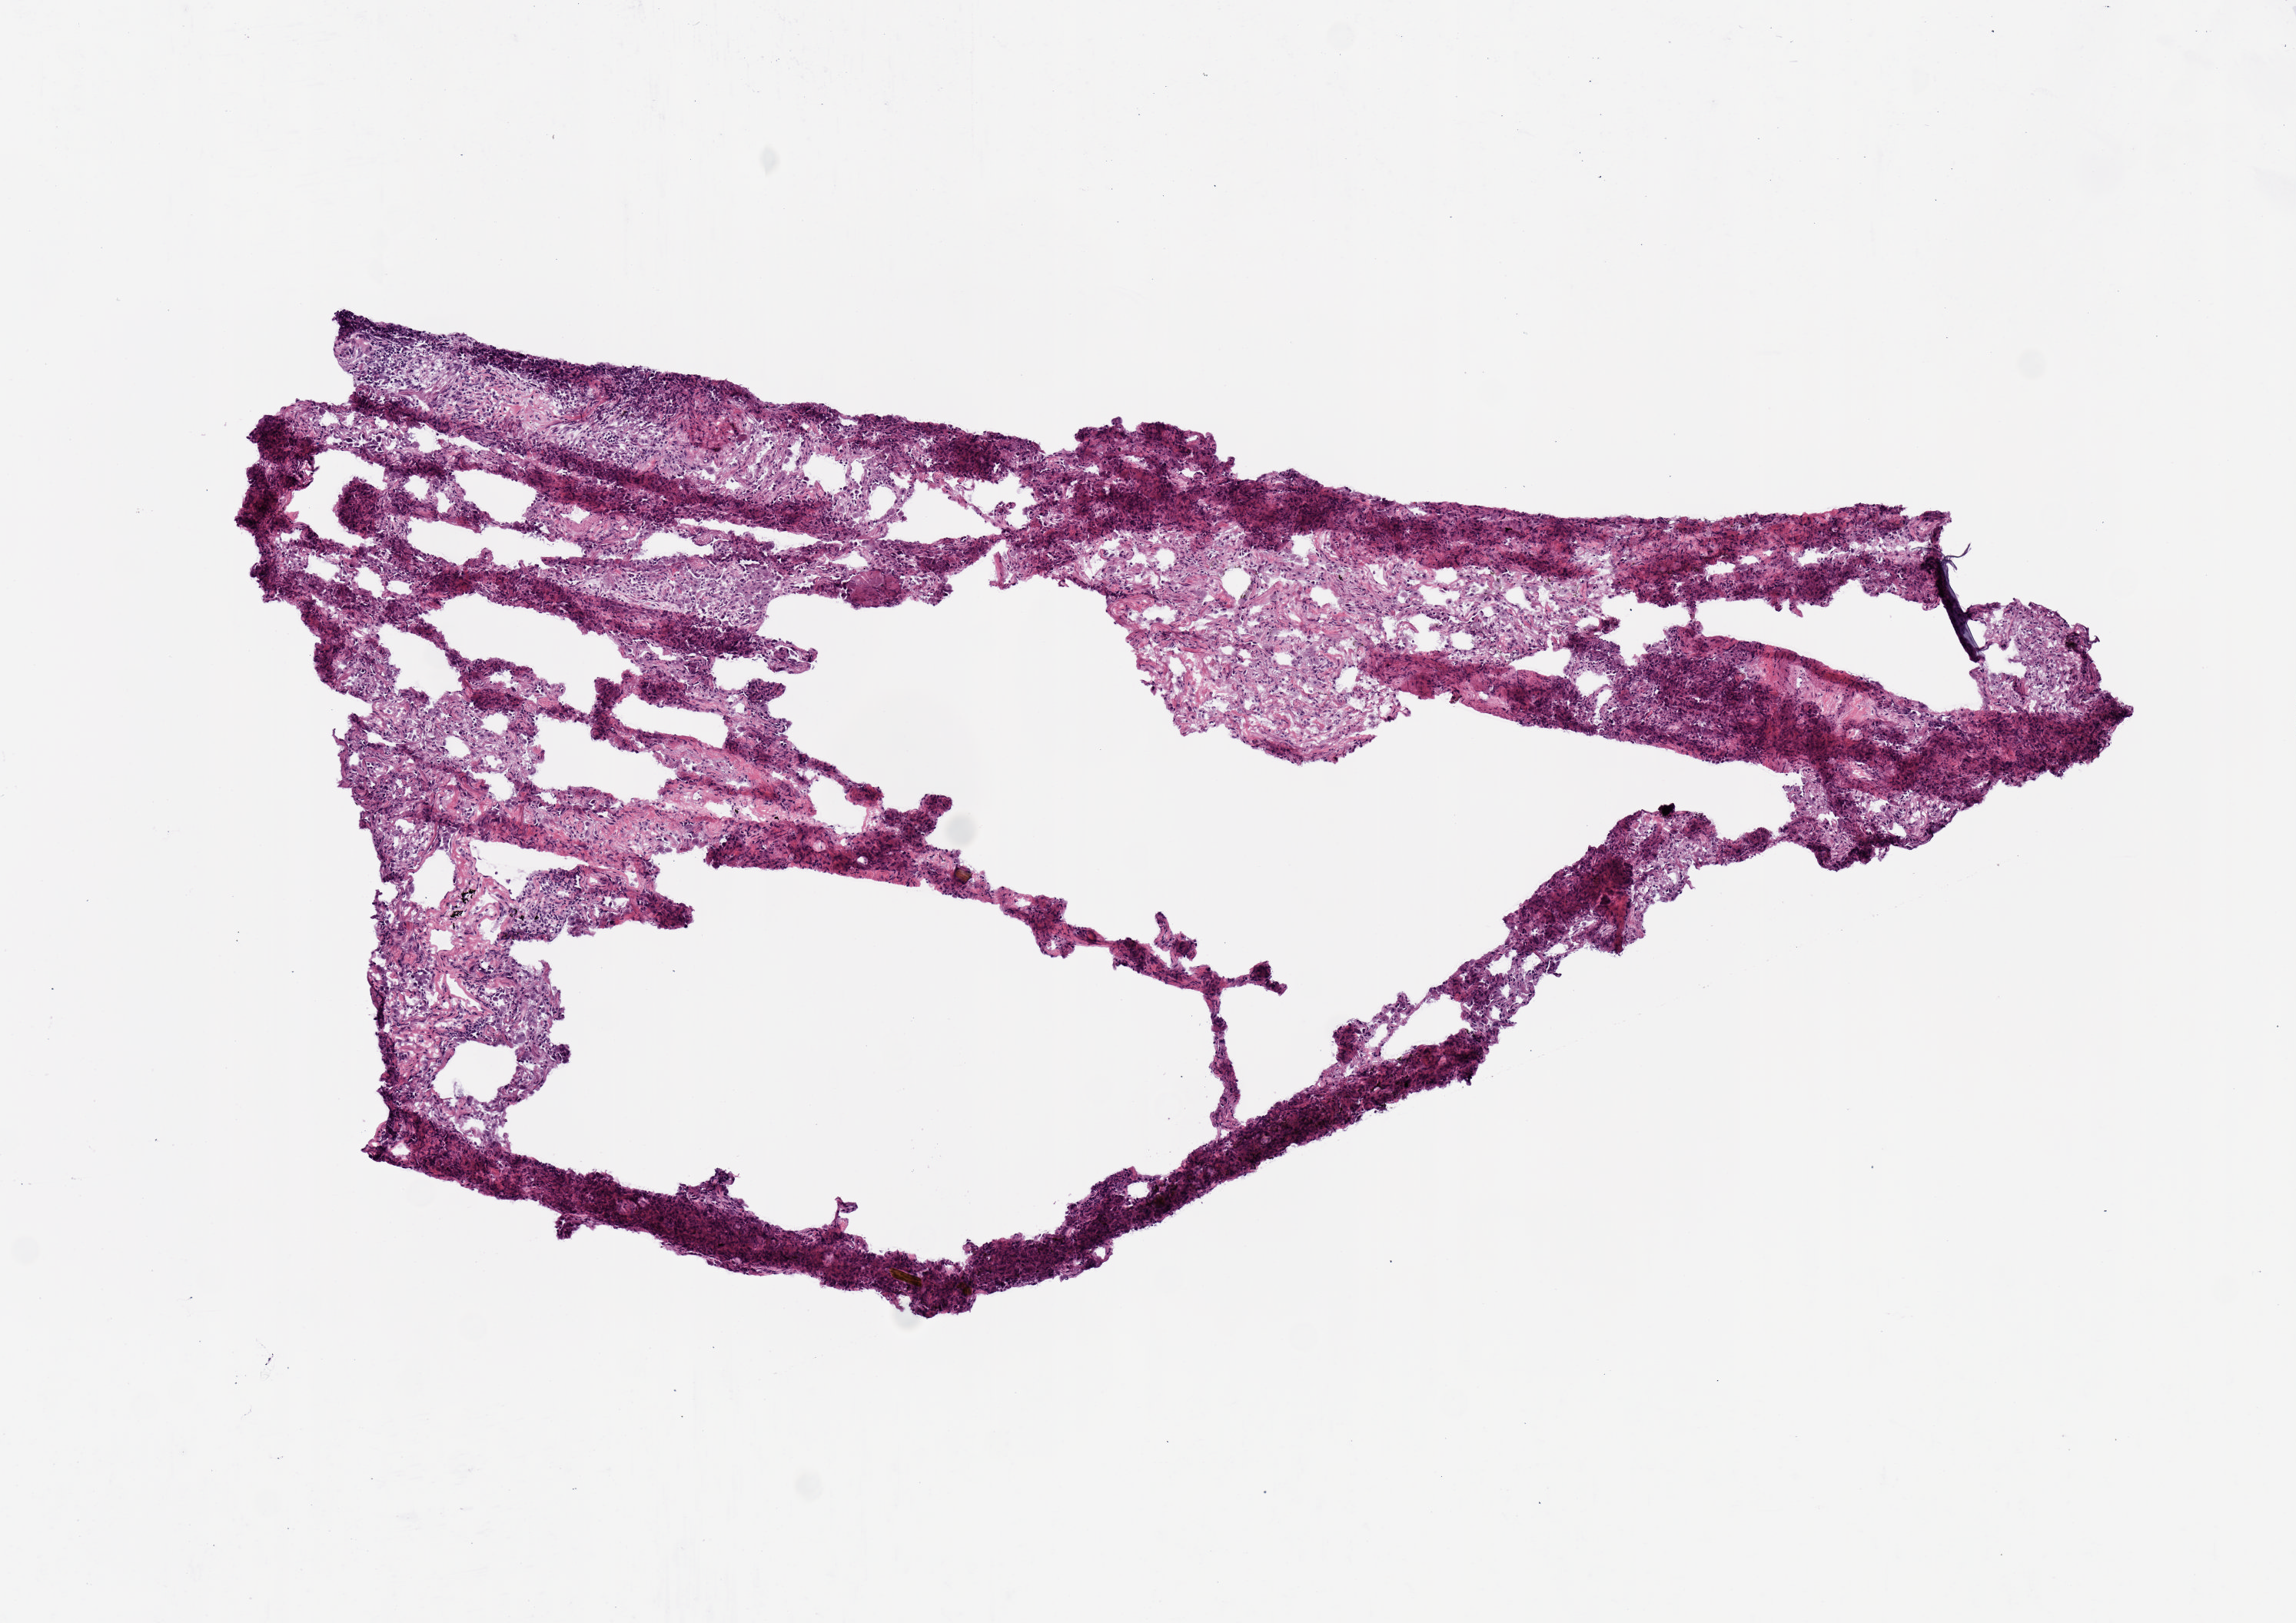
Whole-slide histology image, H&E-stained, whole scanned area (about 5.9 x 4.2 mm, slide scanned at 20x) shown as a low-resolution overview. Frozen section from the top of the tissue portion. Lung, solid tissue normal (non-tumour tissue) sample. Patient: male, age at initial diagnosis 81 years.
* this section: solid tissue normal (non-tumour) sample from the same patient
* patient diagnosis: Mucinous adenocarcinoma (lower lobe, lung)